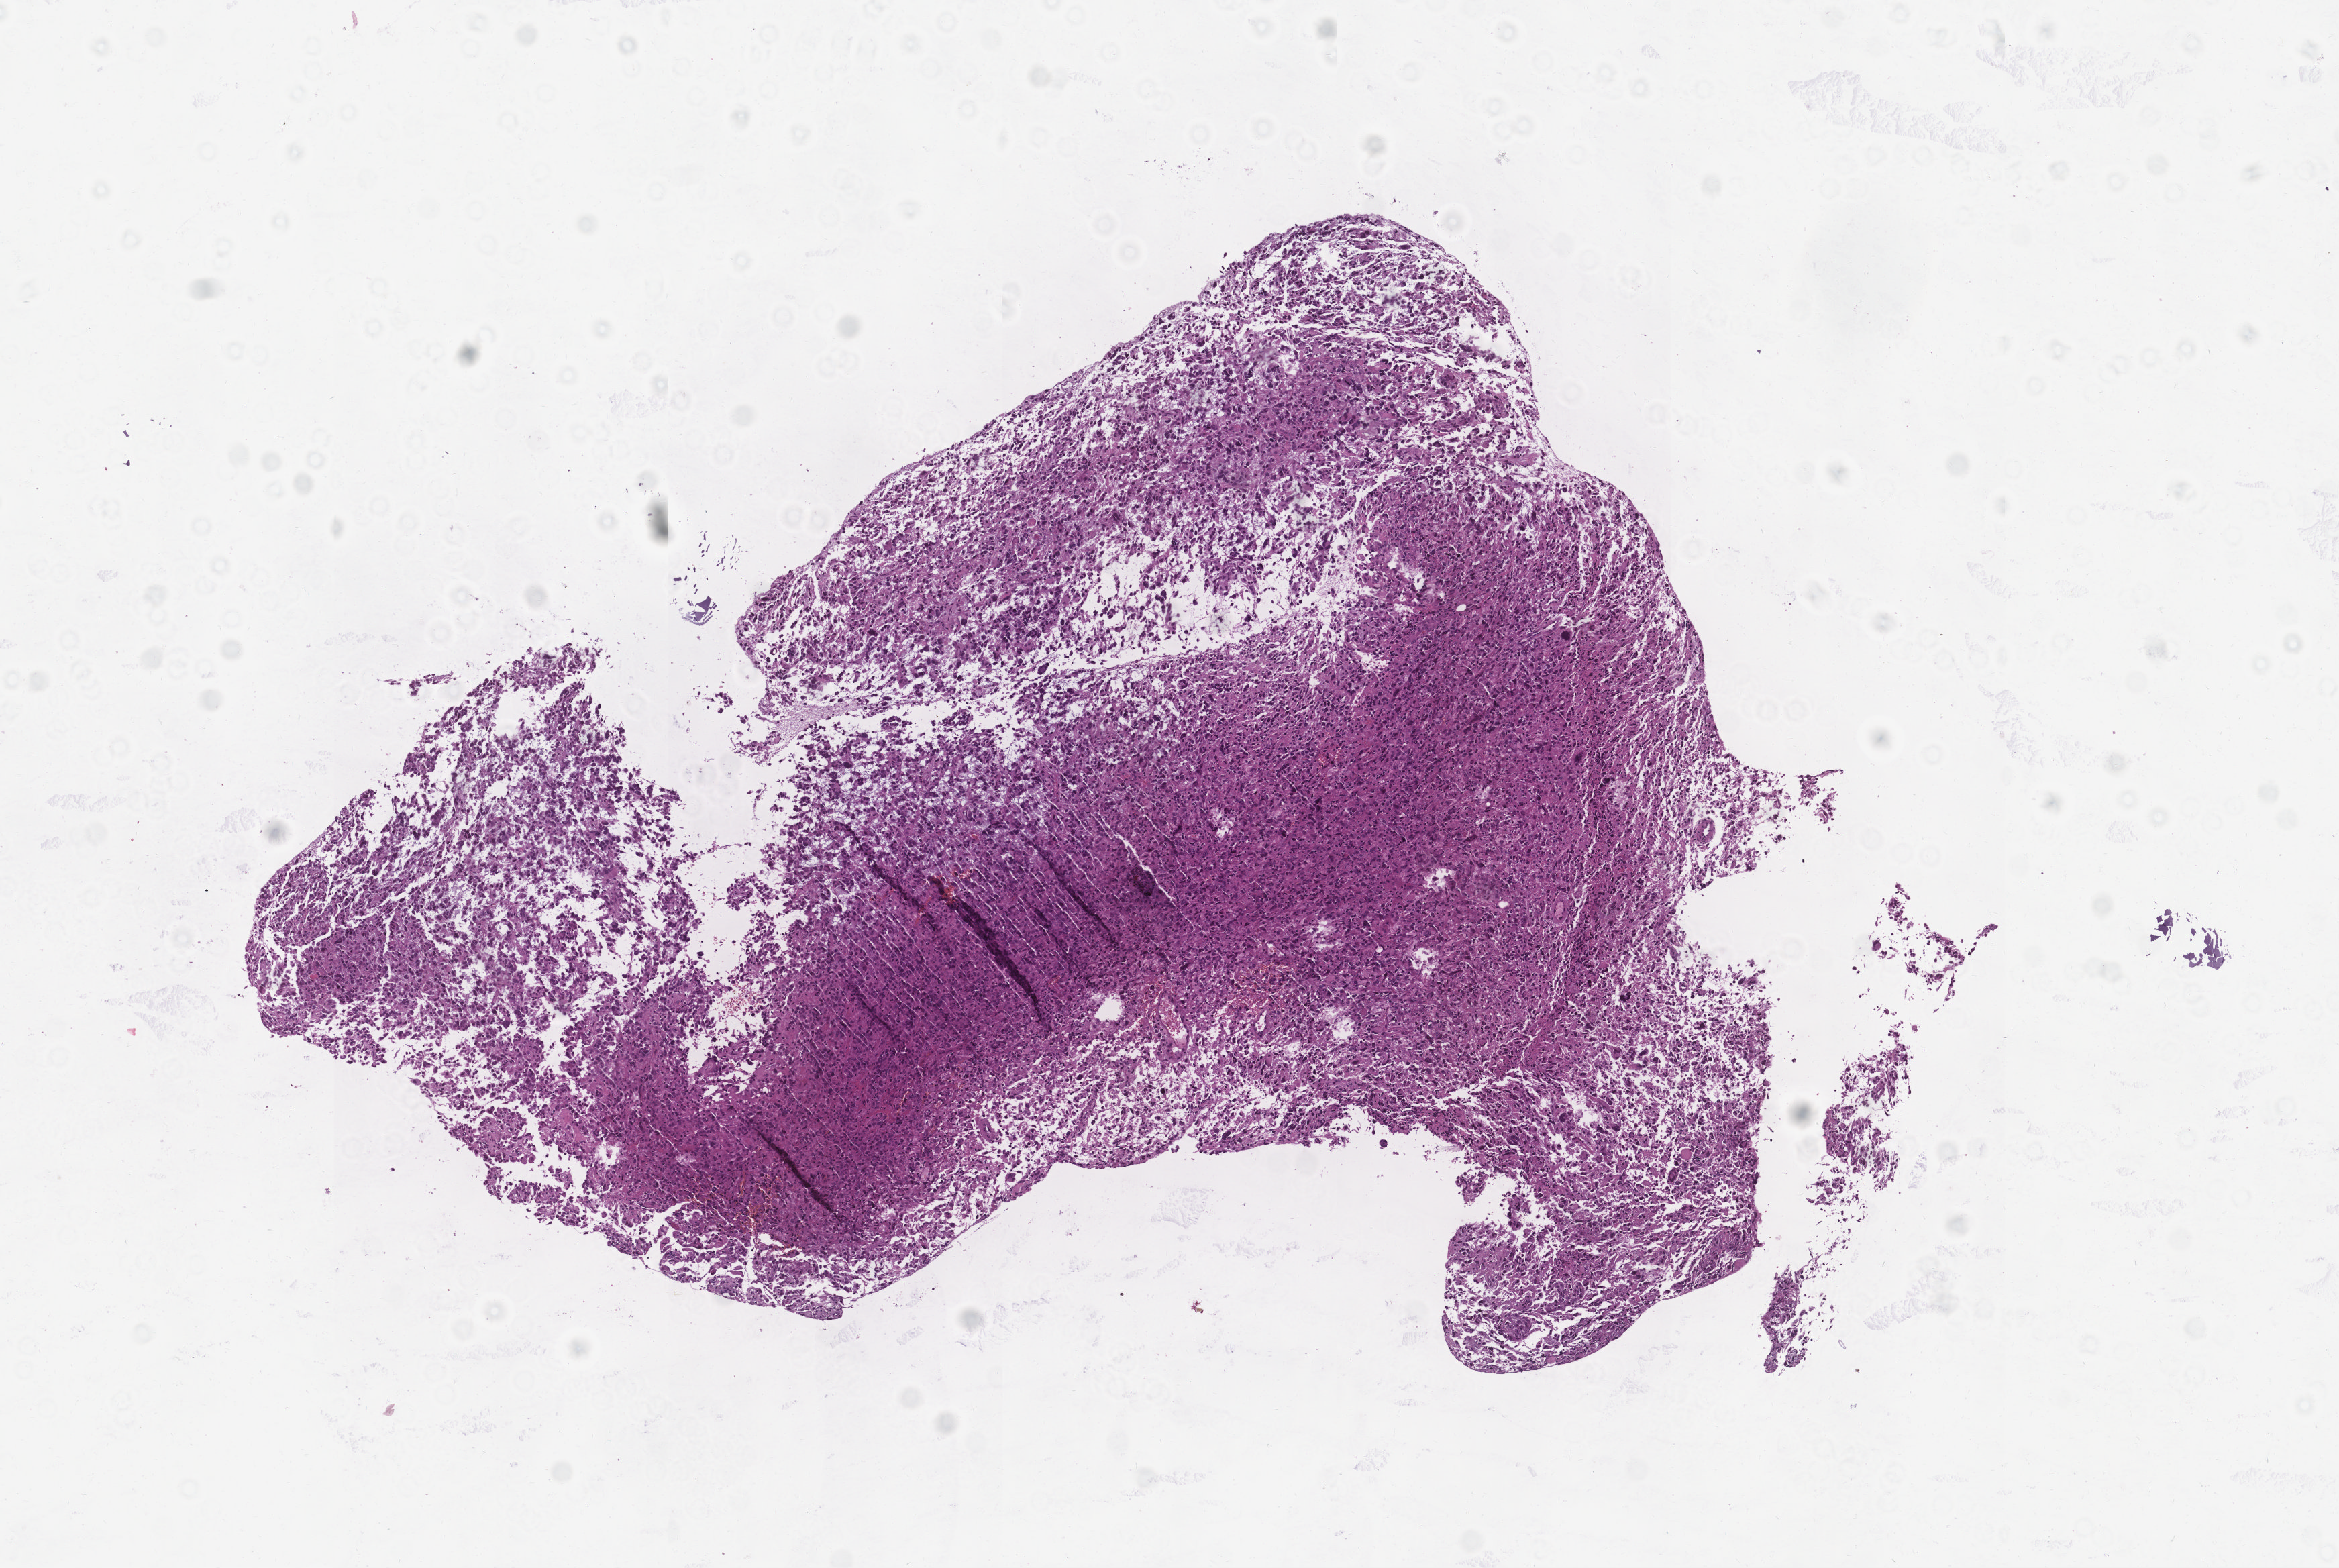
Whole-slide histology image, Hematoxylin and eosin (H&E) stained, a low-resolution overview of the entire scanned area, about 7.0 x 4.7 mm; tumour tissue sample, sampled site: brain. Patient: male, age 71 years. Pathologist review of this section (percent, as recorded): tumour nuclei 85%, necrosis 5%.
Primary tumour site (as recorded): temporal lobe. Histologic diagnosis: Glioblastoma.